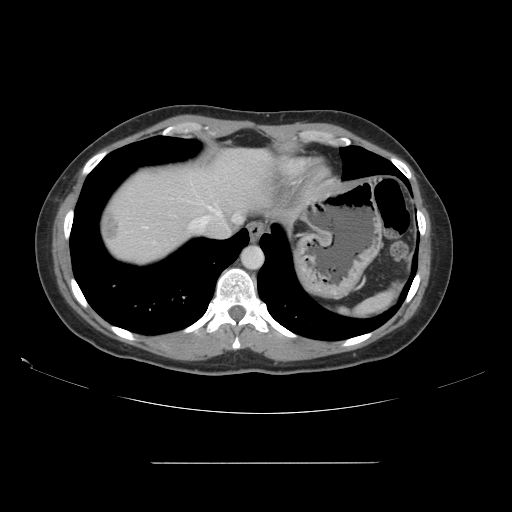
Contrast-enhanced abdominal CT, one axial slice. Position 135 of 151 along the scan axis. 120 kVp. Intravenous contrast given. Soft-tissue window (W 400 / L 40 HU). 2.5 mm slice thickness. 512 × 512 image matrix, field of view 421 × 421 mm. Female patient, age 46 years. Case-level facts recorded for this patient, not image findings: diagnosis: colorectal cancer liver metastases, imaged before liver resection; multiple liver metastases: yes; largest metastasis: 3 cm; disease in both lobes: yes.
Outlined on this slice (outlined manually by an expert reader):
- hepatic veins: box from (x=191, y=207) to (x=240, y=228) px
- liver: (x=99, y=150)–(x=271, y=263)
- planned liver remnant (the part of the liver to remain after resection): (x=113, y=150)–(x=272, y=233)
- liver metastasis: (x=102, y=207)–(x=121, y=245)